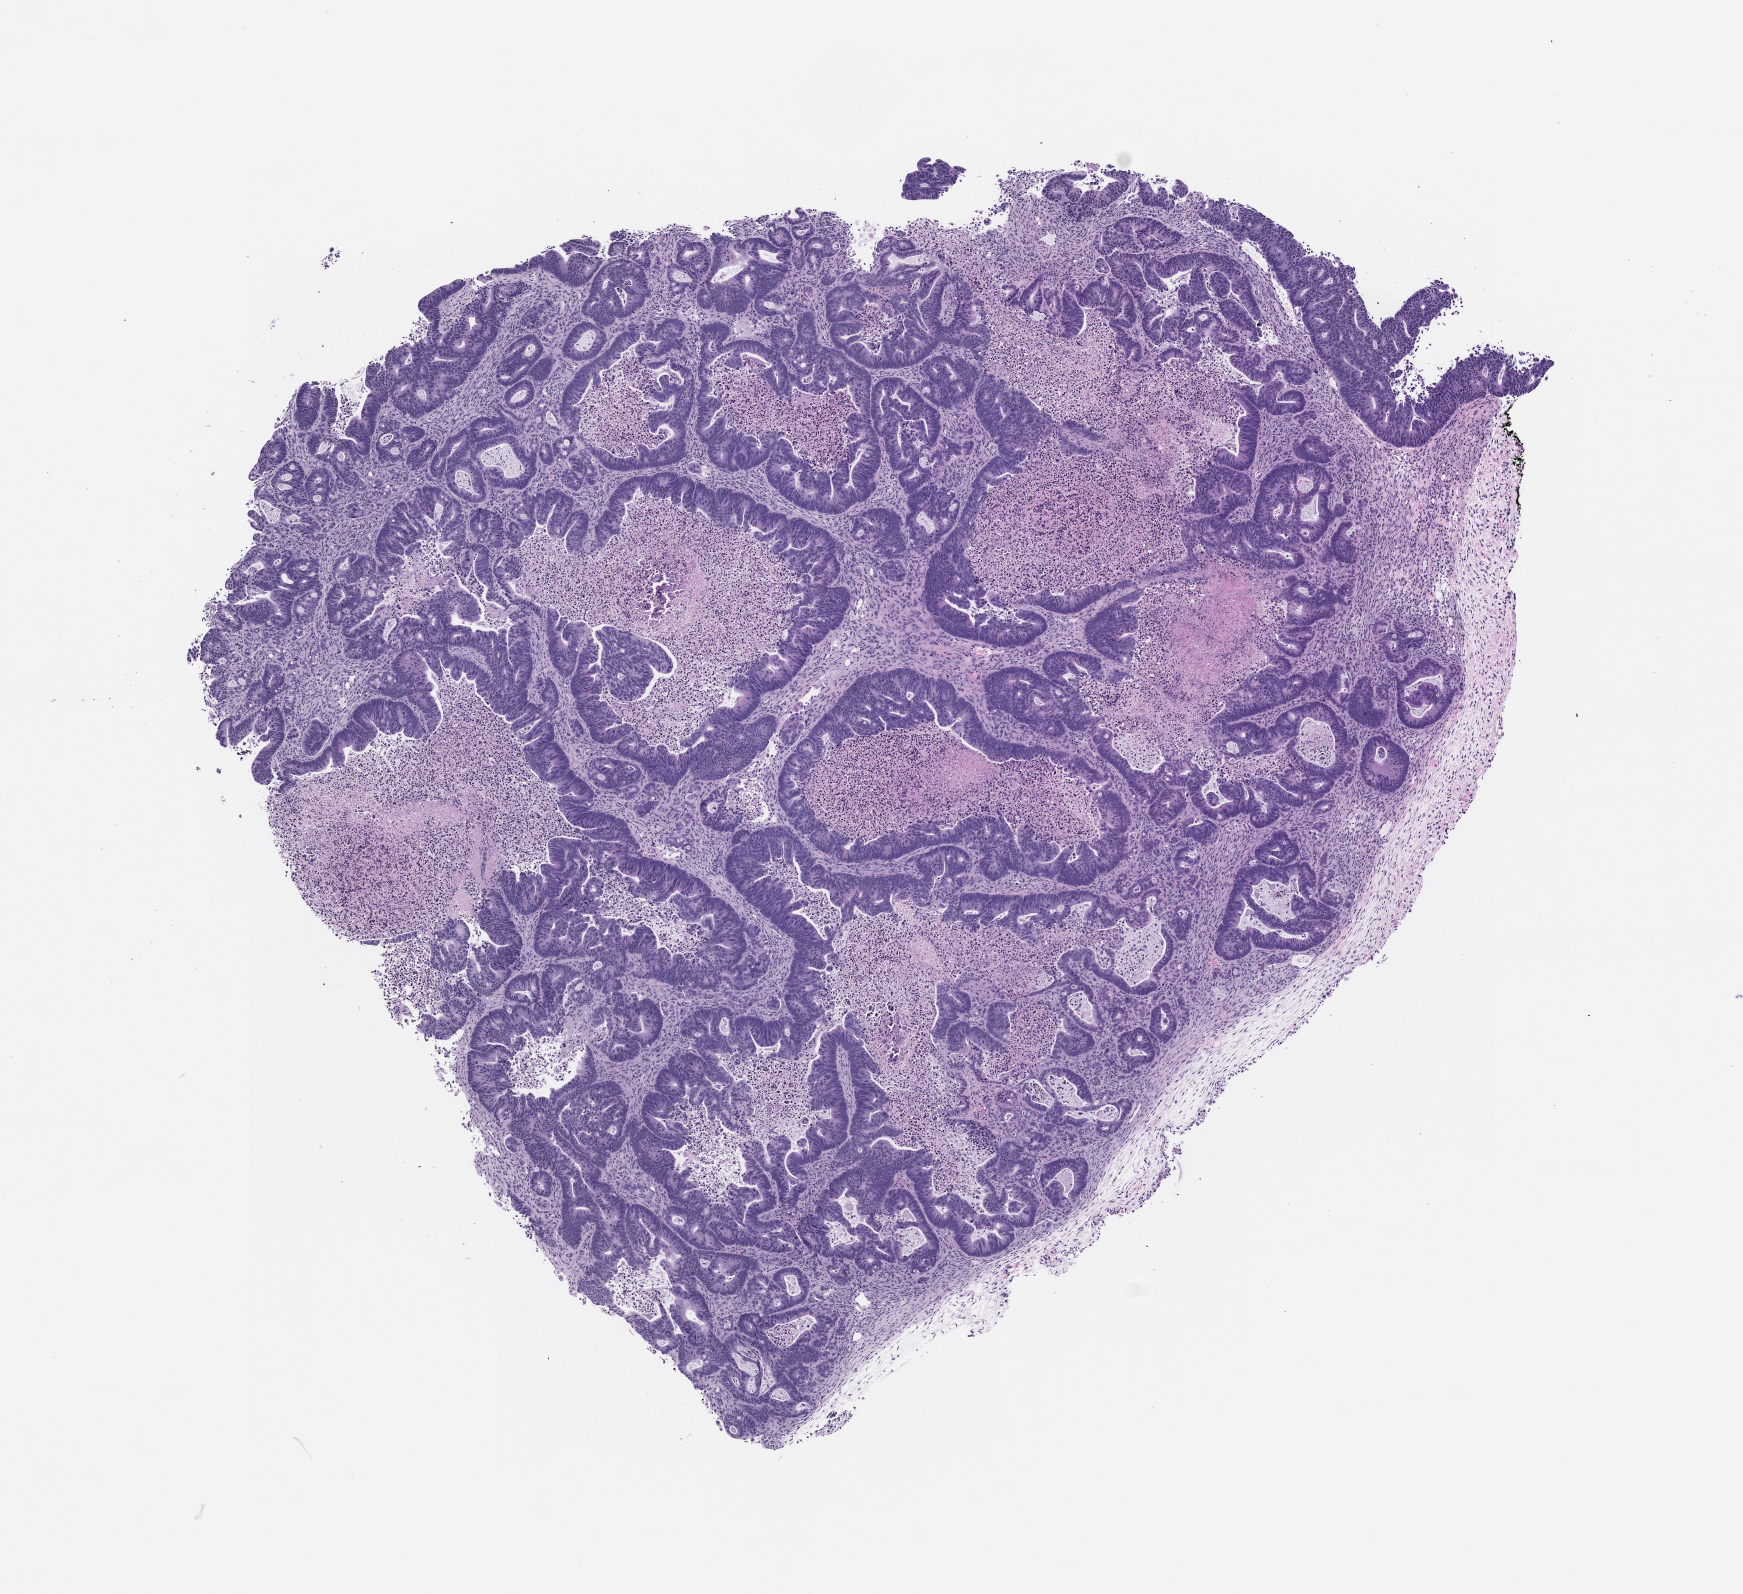
H&E whole-slide image of a patient-derived xenograft (PDX) tumor grown in a mouse, passage 0 — low-resolution overview of the scanned area, about 7.0 x 6.4 mm. Formalin-fixed, paraffin-embedded (FFPE) tissue. Tumor site category: rectum.
Originating patient diagnosis: Rectal Adenocarcinoma.